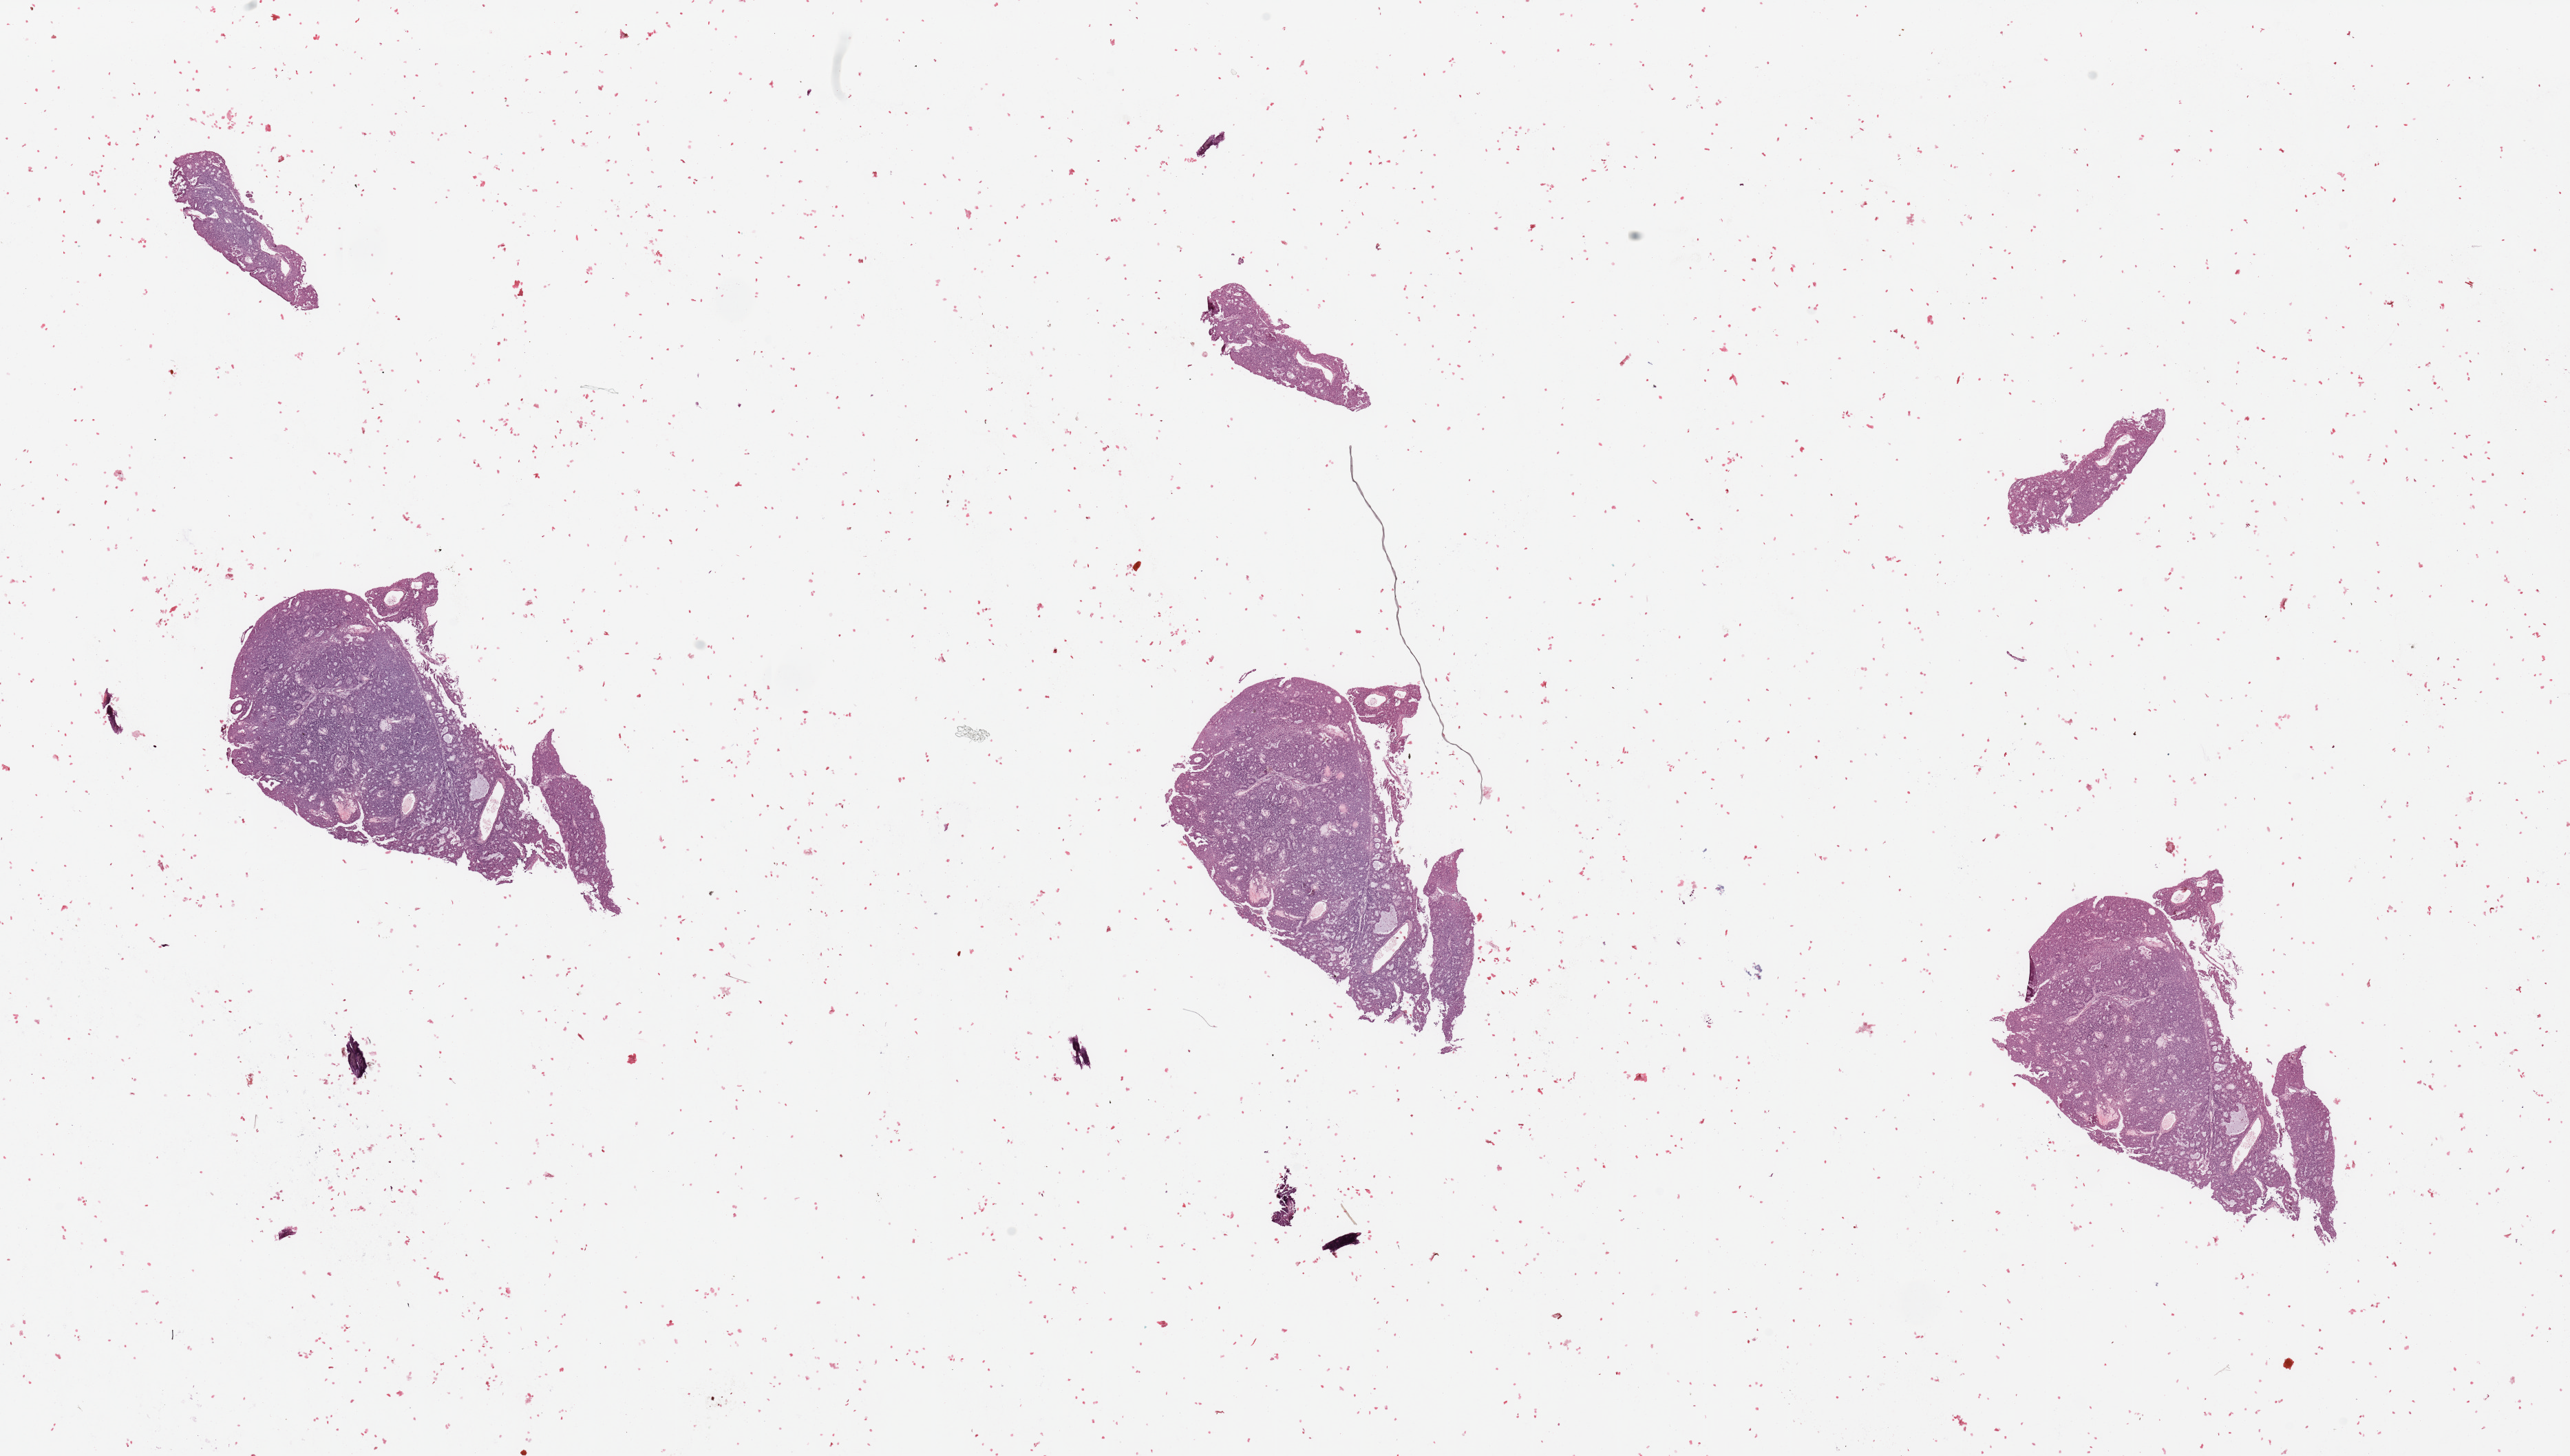
Hematoxylin and eosin (H&E) stained whole-slide image — shown as a low-resolution overview of the whole scanned area (about 29.5 x 16.7 mm, acquisition: 20x scan). Tumour tissue sample, sampled site: uterus. 56-year-old female patient. Histologic grade: G3 (poorly differentiated). Composition of this section per pathologist review: tumour nuclei 95%, necrosis 2%.
AJCC pathologic stage: IIIC1. Diagnosis: Endometrioid adenocarcinoma, NOS. Primary tumour site (as recorded): anterior endometrium.